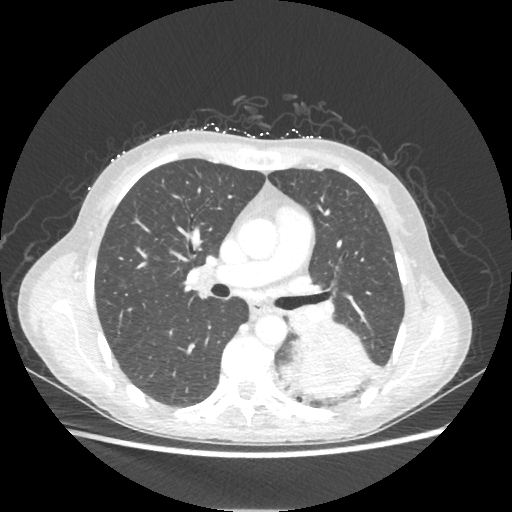
Chest CT, one axial slice. Slice 124 of 221 in the series (ordered by position). Reconstruction kernel STANDARD. Lung window (W 1500 / L -600 HU). 1.25 mm slice thickness. 512 × 512 image matrix, field of view 360 × 360 mm. Female patient, age 53 years. From the clinical record (not read from this slice): clinical TNM (as recorded): T3 N0 M0.
Structures marked on this image (bounding box drawn by a radiologist):
- lung tumour (recorded histology: adenocarcinoma): bounding box <284,320,369,400> (left, top, right, bottom; pixels)